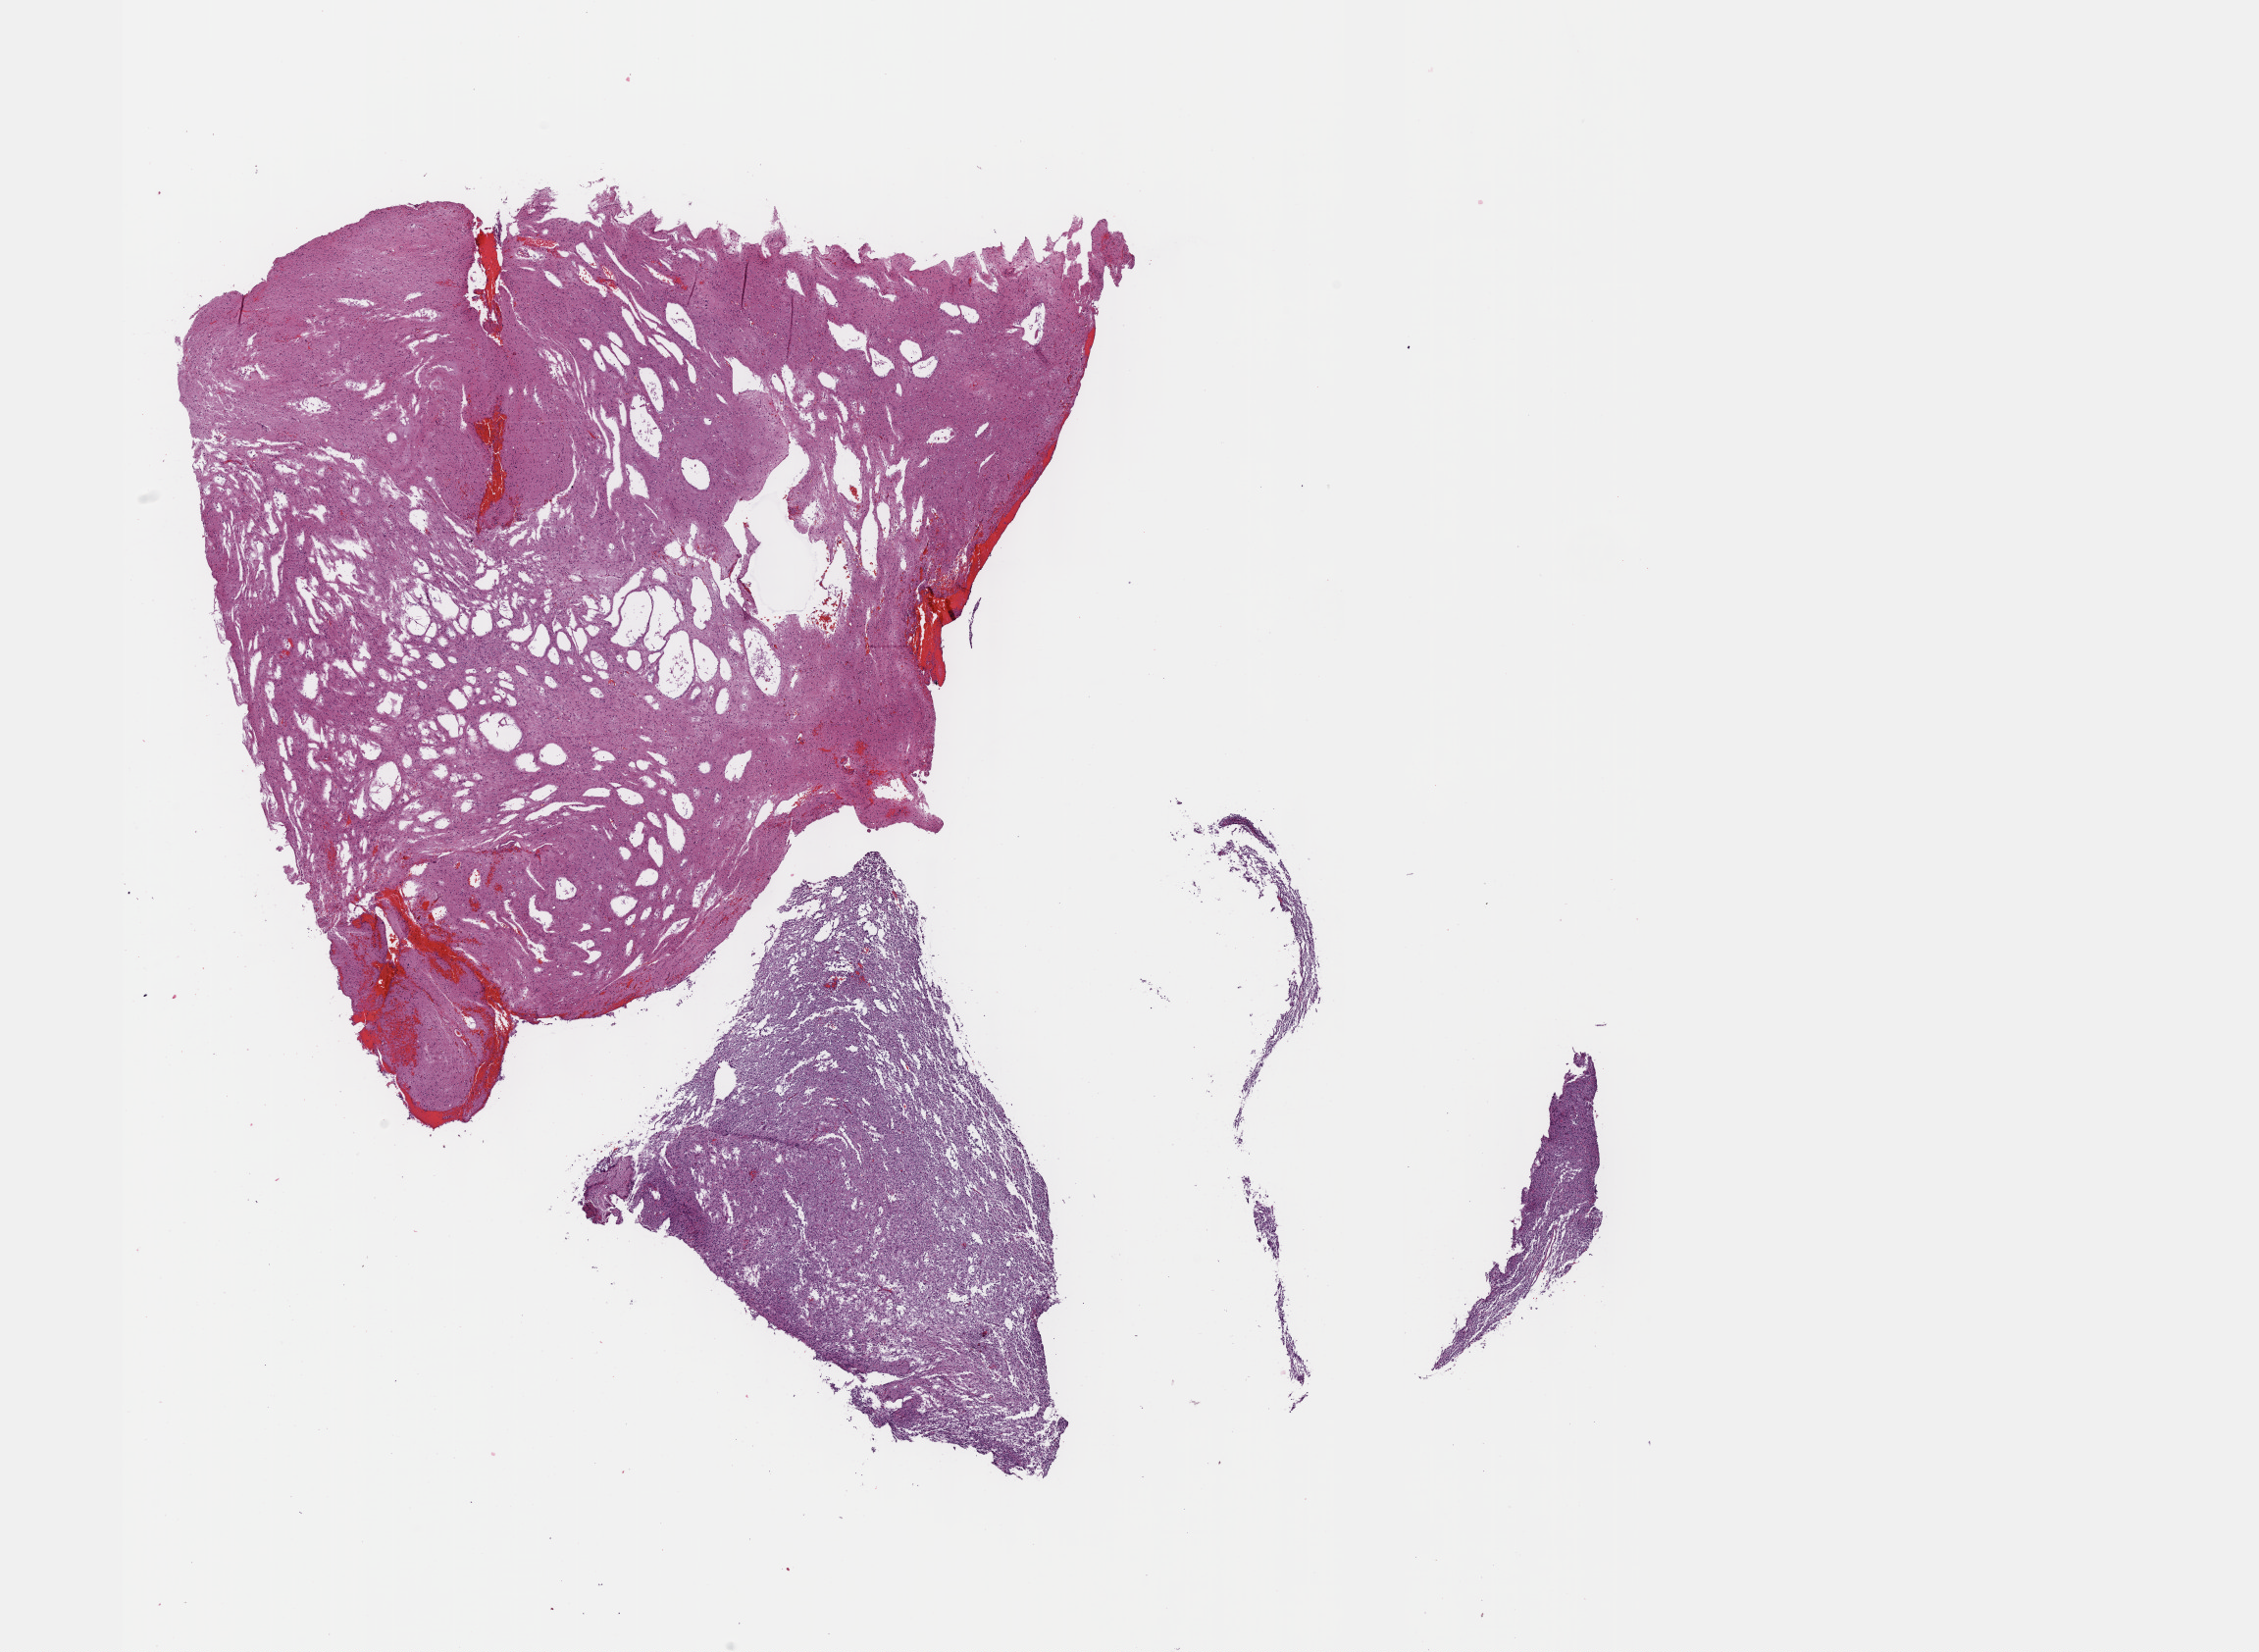
Digitized Hematoxylin and eosin (H&E) stained tissue section (whole slide) — a low-resolution overview of the entire scanned area, about 18.6 x 13.6 mm (from a 40x scan). FFPE section. Sample: primary tumour, brain. Male patient; age at initial diagnosis 60 years.
Diagnosis: Oligodendroglioma, anaplastic (cerebrum).